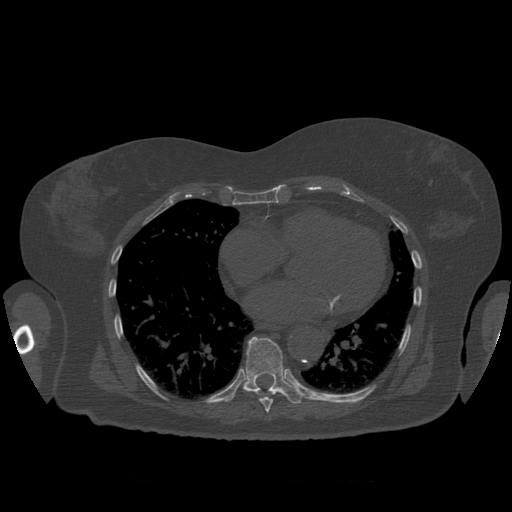
CT including the spine, one axial slice. Slice 367 of 399 in the series (ordered by position). 120 kVp. Bone window (W 1800 / L 400 HU). 1.25 mm slice thickness. 512 × 512 image matrix. Patient age 81 years. Case-level facts recorded for this patient, not image findings: primary cancer: renal; vertebrae with lytic lesions (as recorded): L1.
Structures marked on this image (semi-automatic segmentation, software-assisted and operator-edited):
- T8 vertebra: bounding box (x1, y1, x2, y2) in pixels: (246, 391, 273, 413)
- T9 vertebra: (243, 337, 303, 404)